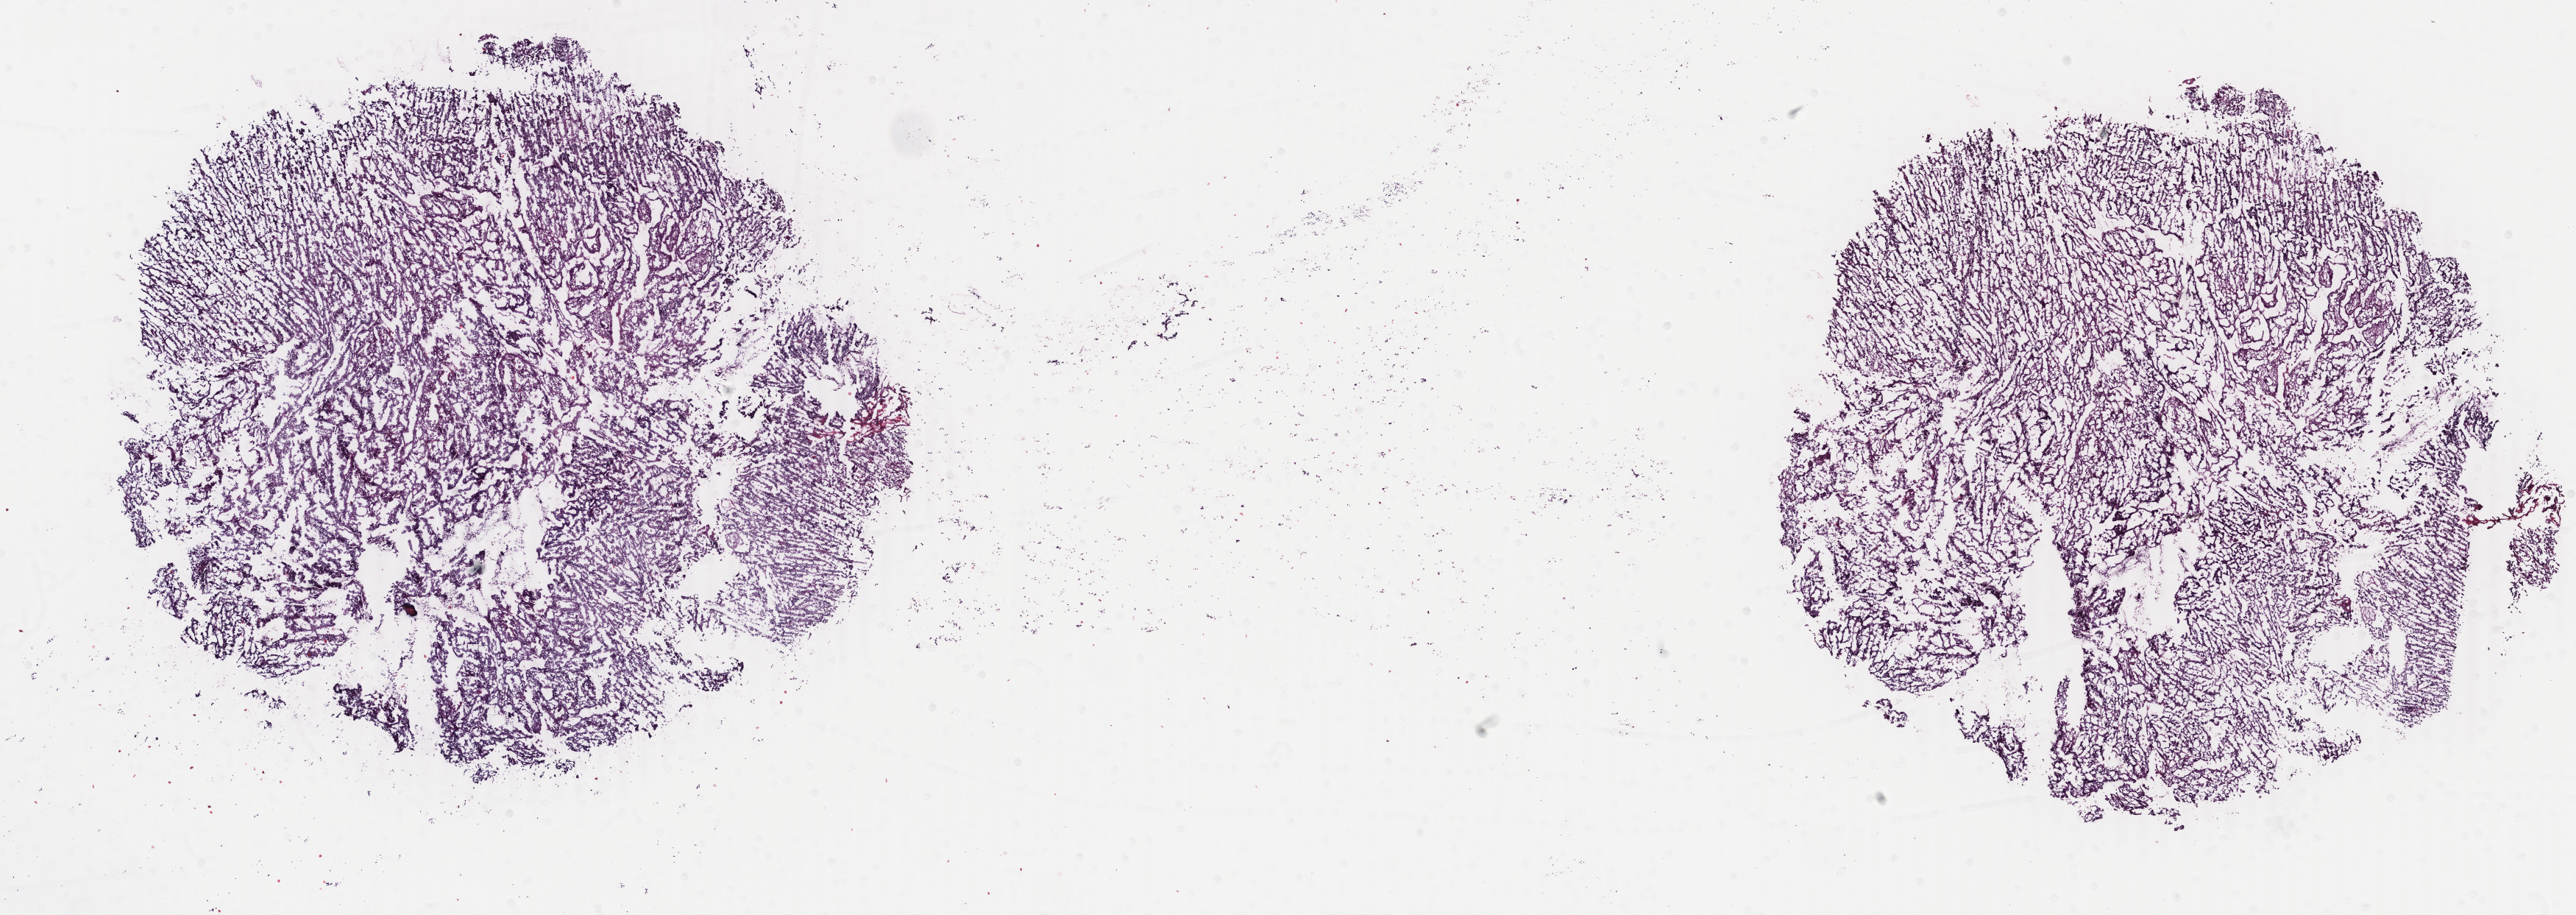
Whole-slide histology image, Hematoxylin and eosin (H&E) stained, a low-resolution overview of the entire scanned area, about 27.8 x 9.9 mm. Frozen section from the top of the tissue portion. Sample: primary tumour, uterus. Female, age 59 years at initial diagnosis. Histologic grade: G2 (moderately differentiated). Slide review estimates, as recorded: tumour cells 100%, tumour nuclei 90%, normal cells 0%, stromal cells 0%, necrosis 0%. Infiltration values recorded for this section: lymphocyte infiltration 0%, monocyte infiltration 0%, neutrophil infiltration 0%.
Histologic diagnosis: Endometrioid adenocarcinoma, NOS. FIGO stage: IA.